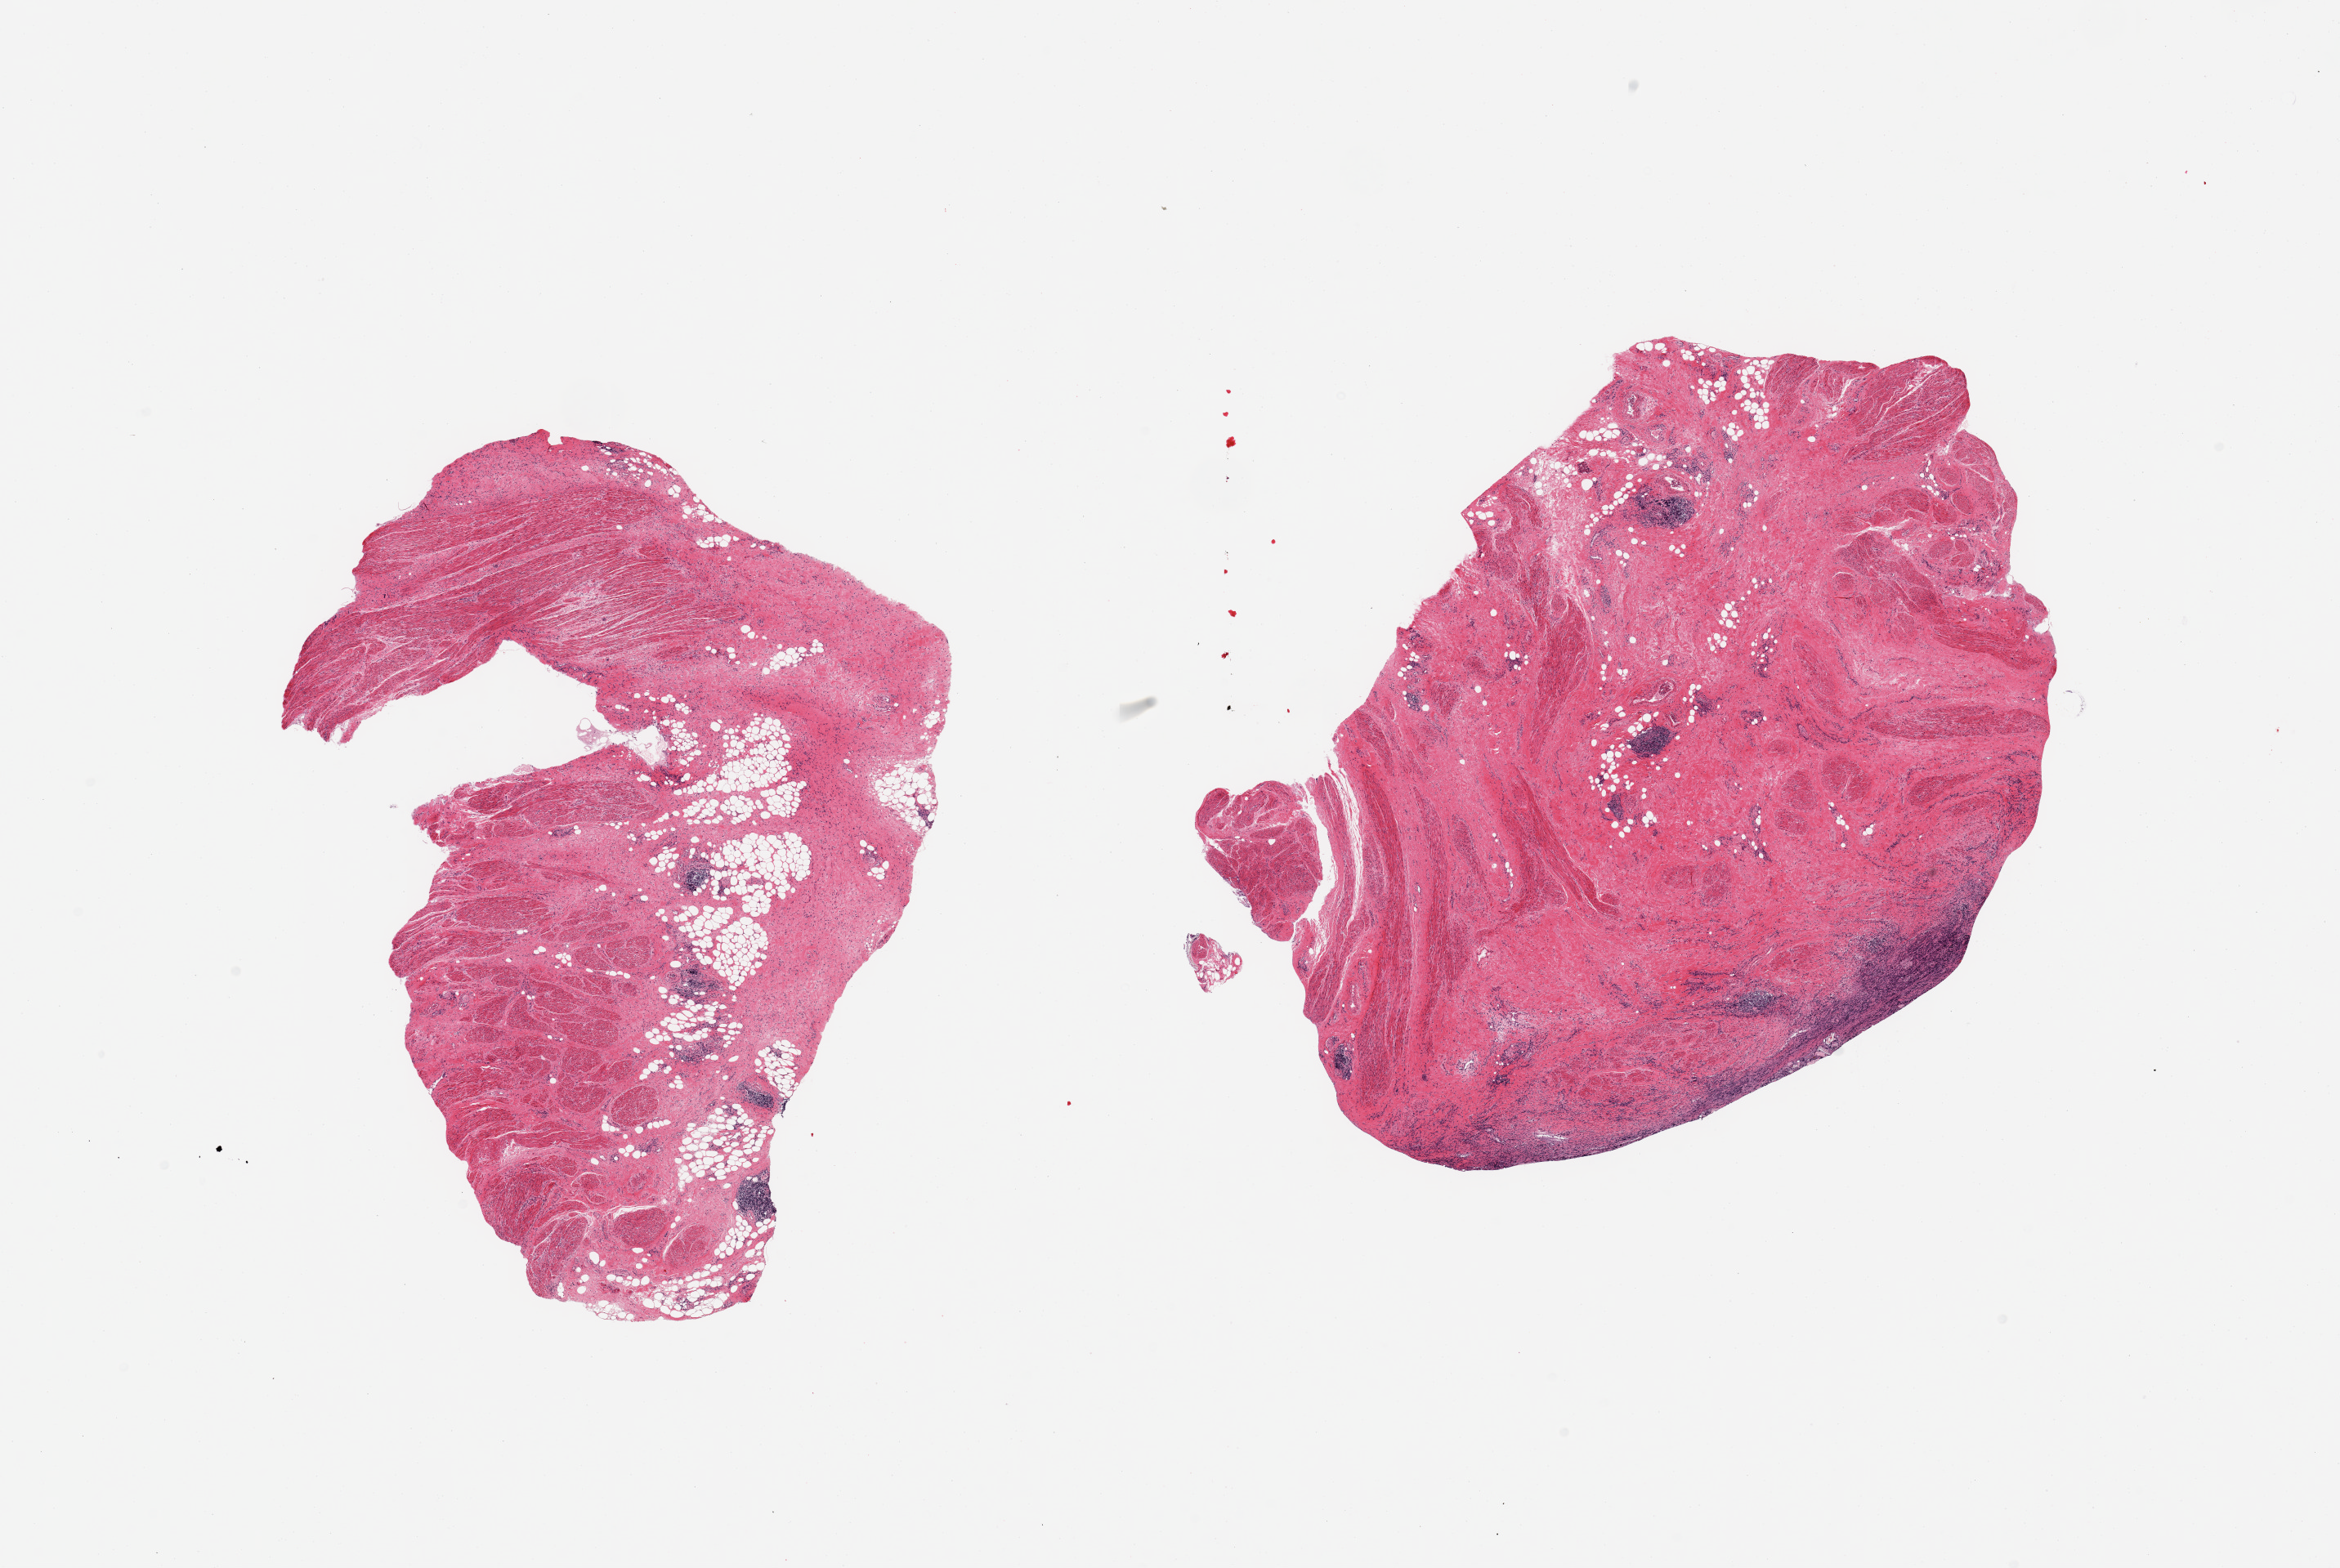
Whole-slide image, hematoxylin and eosin (H&E) stain — shown as a low-resolution overview of the whole scanned area (about 22.6 x 15.2 mm), PAXgene-fixed paraffin-embedded (PFPE) section, section of prostate (target tissue), tissue donor sample. Donor: male.
Pathologist's review note for this sample: 2 pieces; no prostatic glands, only fibromuscular and fatty stroma with chronic inflammation, resembles bladder wall.